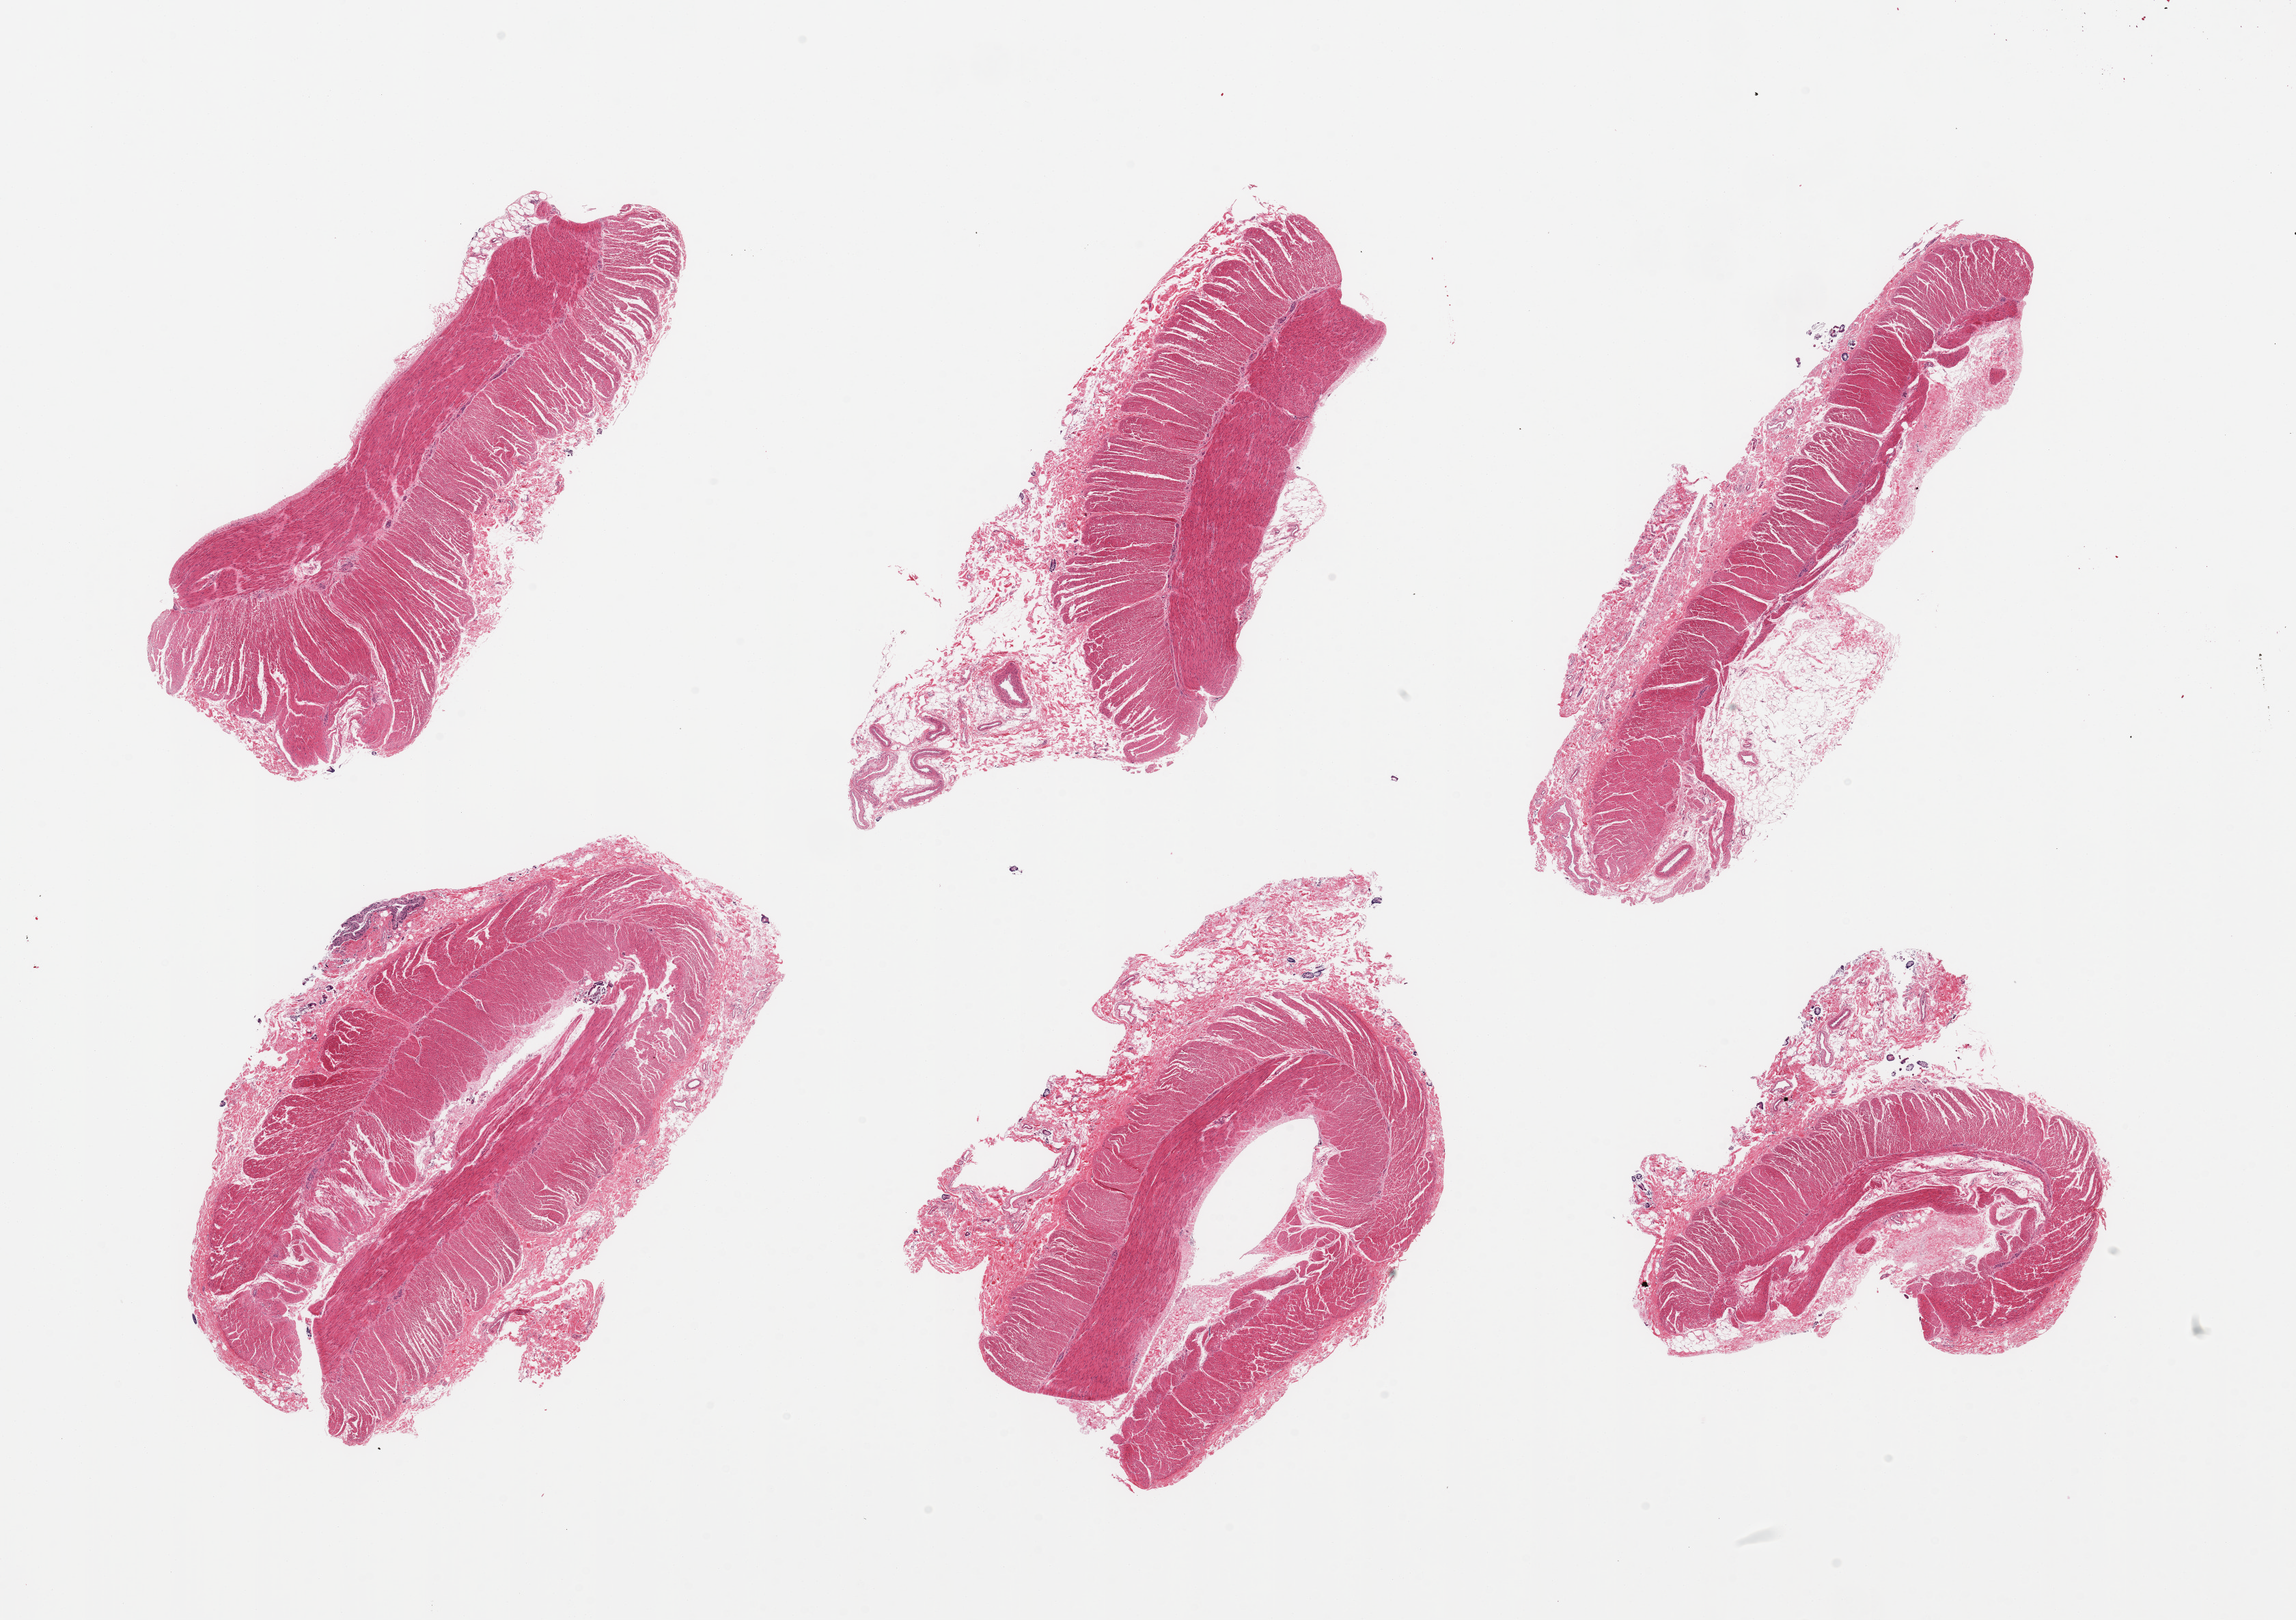
Whole-slide image, haematoxylin and eosin stain, brightfield, low-resolution overview of the scanned area, about 26.6 x 18.8 mm, PAXgene-fixed, paraffin-embedded tissue, section of transverse colon (target tissue), tissue donor sample.
Review note (as recorded): 6 pieces; muscularis only, no mucosa.